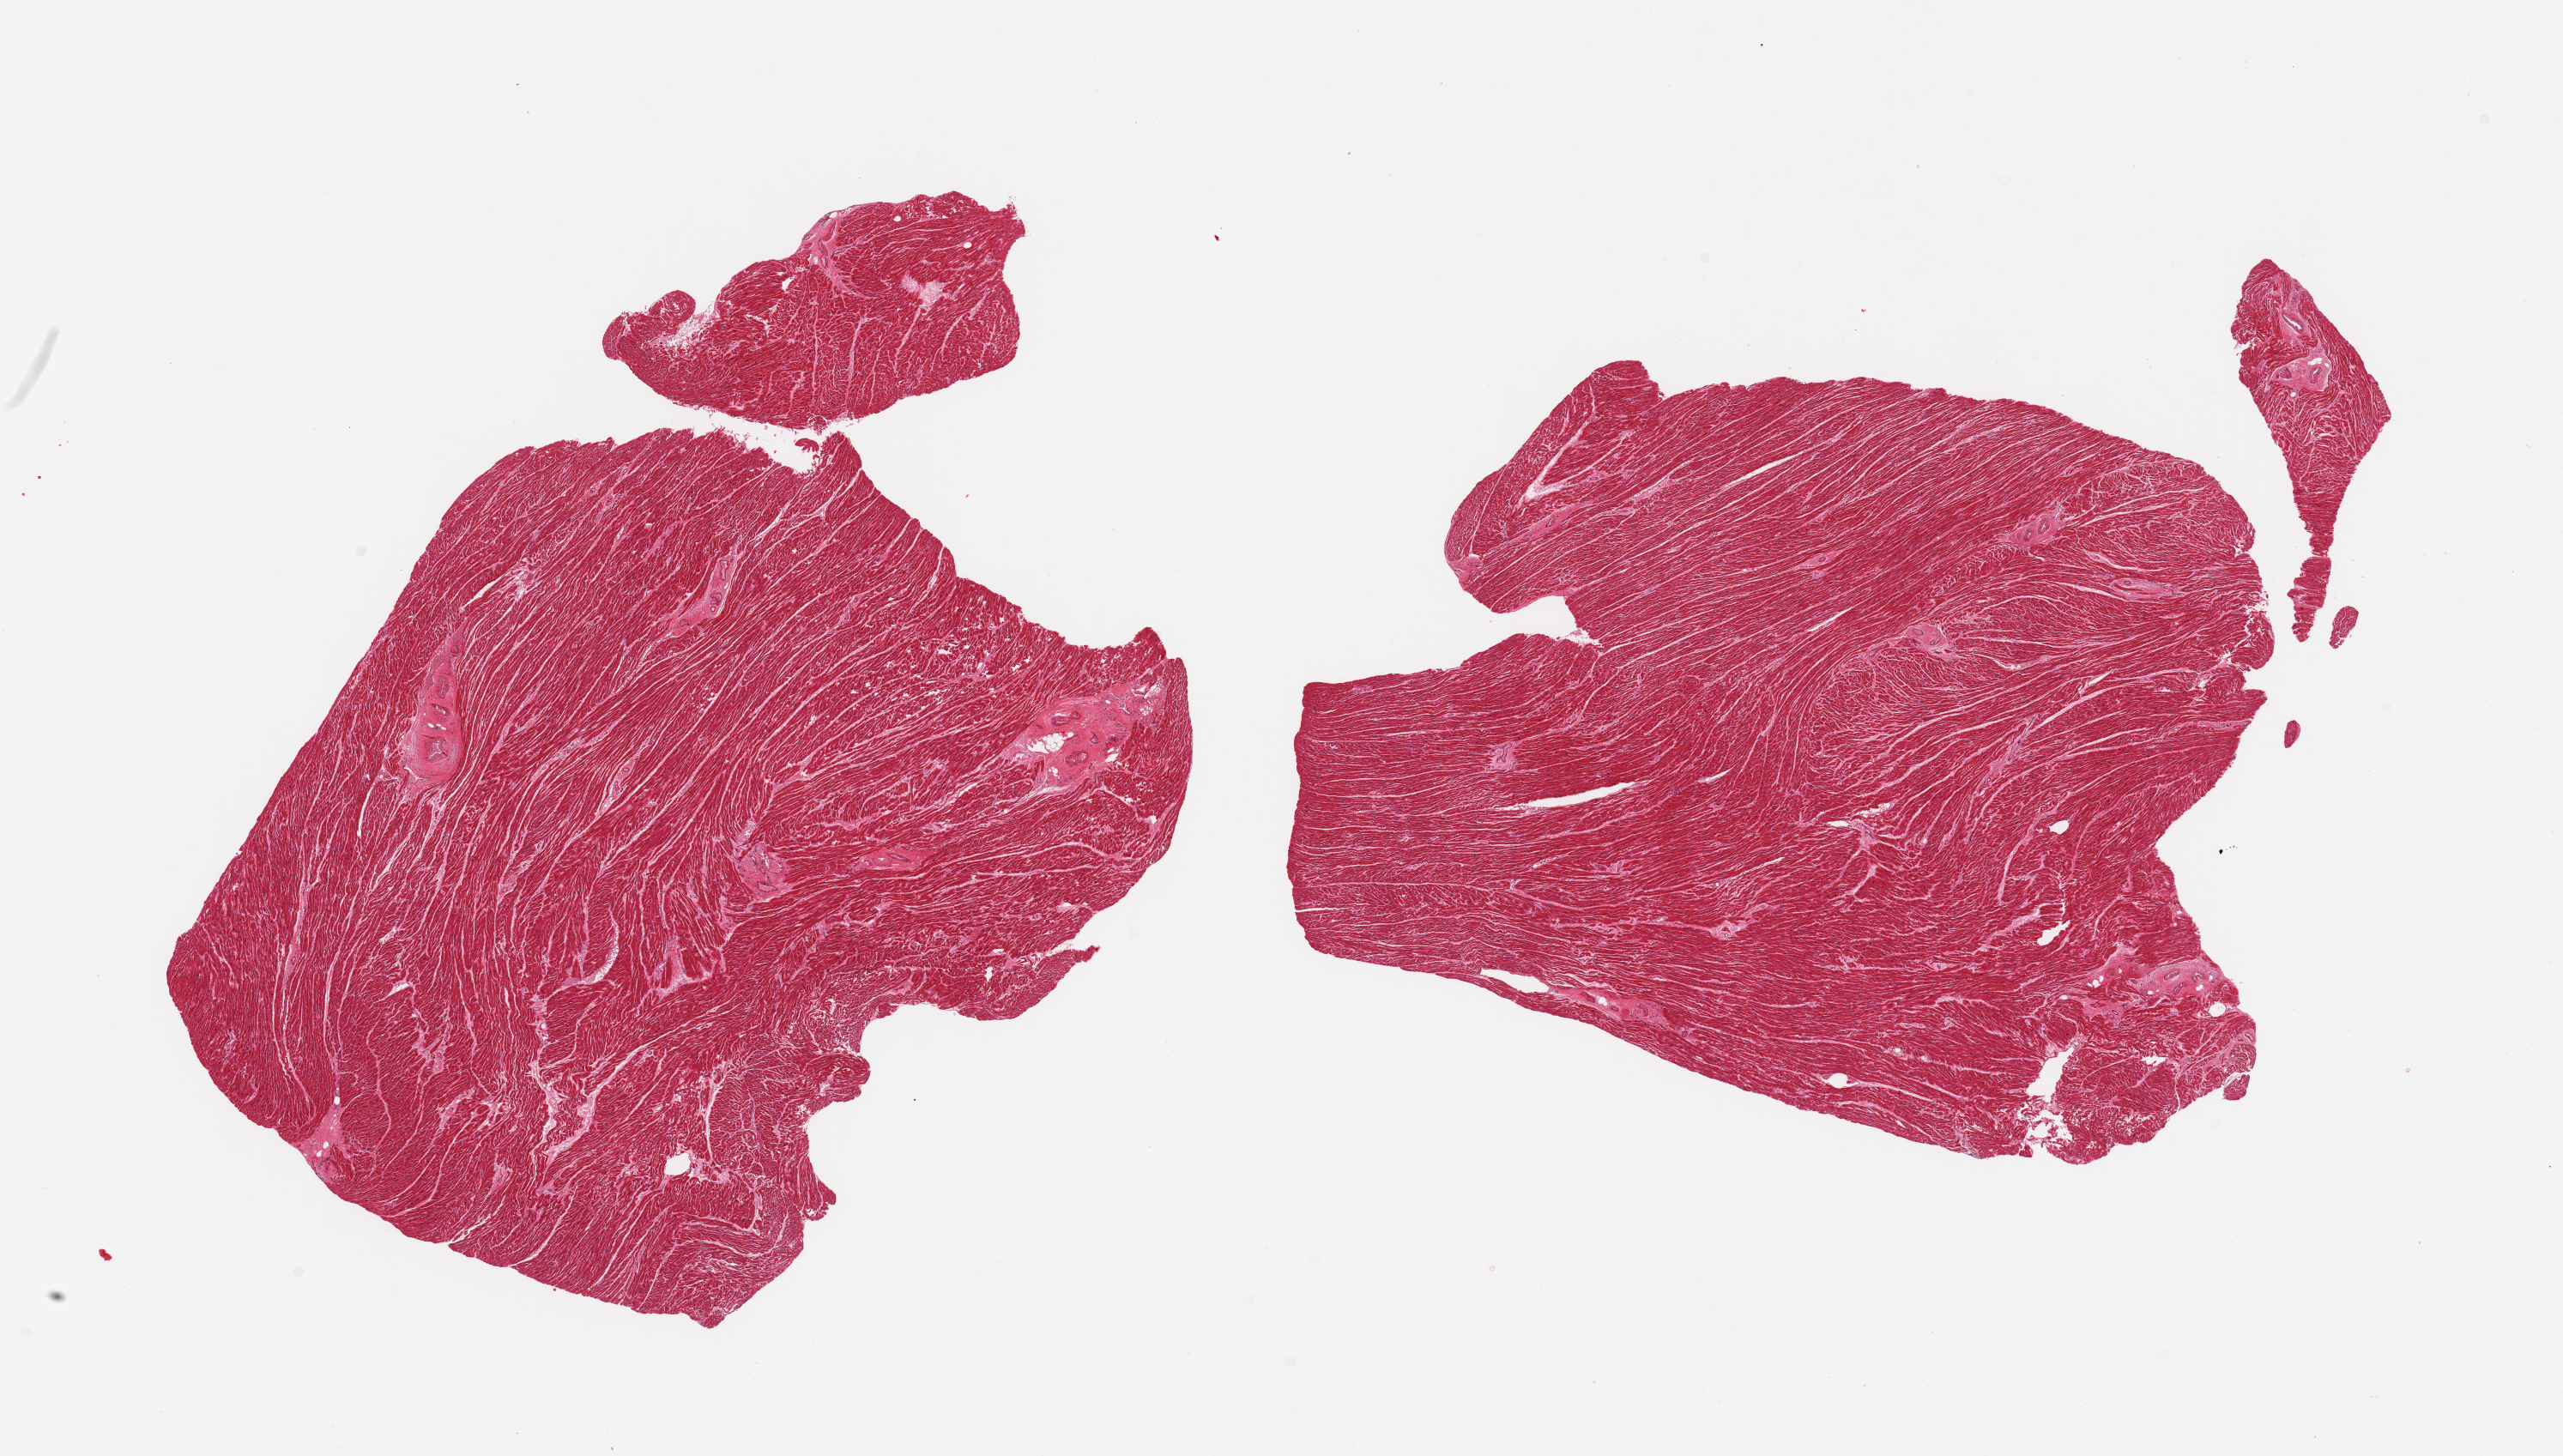
Whole-slide image, hematoxylin and eosin (H&E) stain, shown as a low-resolution overview of the whole scanned area (about 23.6 x 13.4 mm). PAXgene-fixed, paraffin-embedded tissue. Sampled site (target tissue): heart. Tissue donor sample. Donor sex: male.
- reviewer comment on this tissue sample: 2 pieces